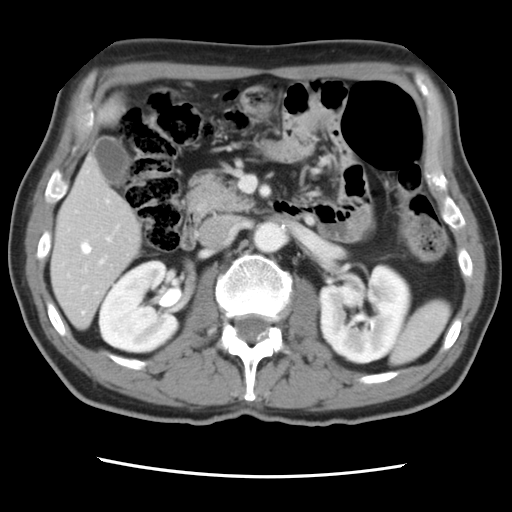
Contrast-enhanced abdominal CT, one axial slice. Slice 36 of 83 in the series (ordered by position). 120 kVp. Intravenous contrast given. Soft-tissue window (W 400 / L 40 HU). 512 × 512 image matrix, field of view 321 × 321 mm. Male patient, age 69 years. From the clinical record (not read from this slice): diagnosis: colorectal cancer liver metastases, imaged before liver resection; multiple liver metastases: yes; largest metastasis: 3.5 cm; chemotherapy before resection: yes.
Annotated regions visible in this slice (expert manual segmentation):
- hepatic veins: bounding box <81,200,109,255> (left, top, right, bottom; pixels)
- liver: <52,104,142,327>
- planned liver remnant (the part of the liver to remain after resection): <52,160,141,327>
- portal vein (with intrahepatic branches): <82,225,119,290>